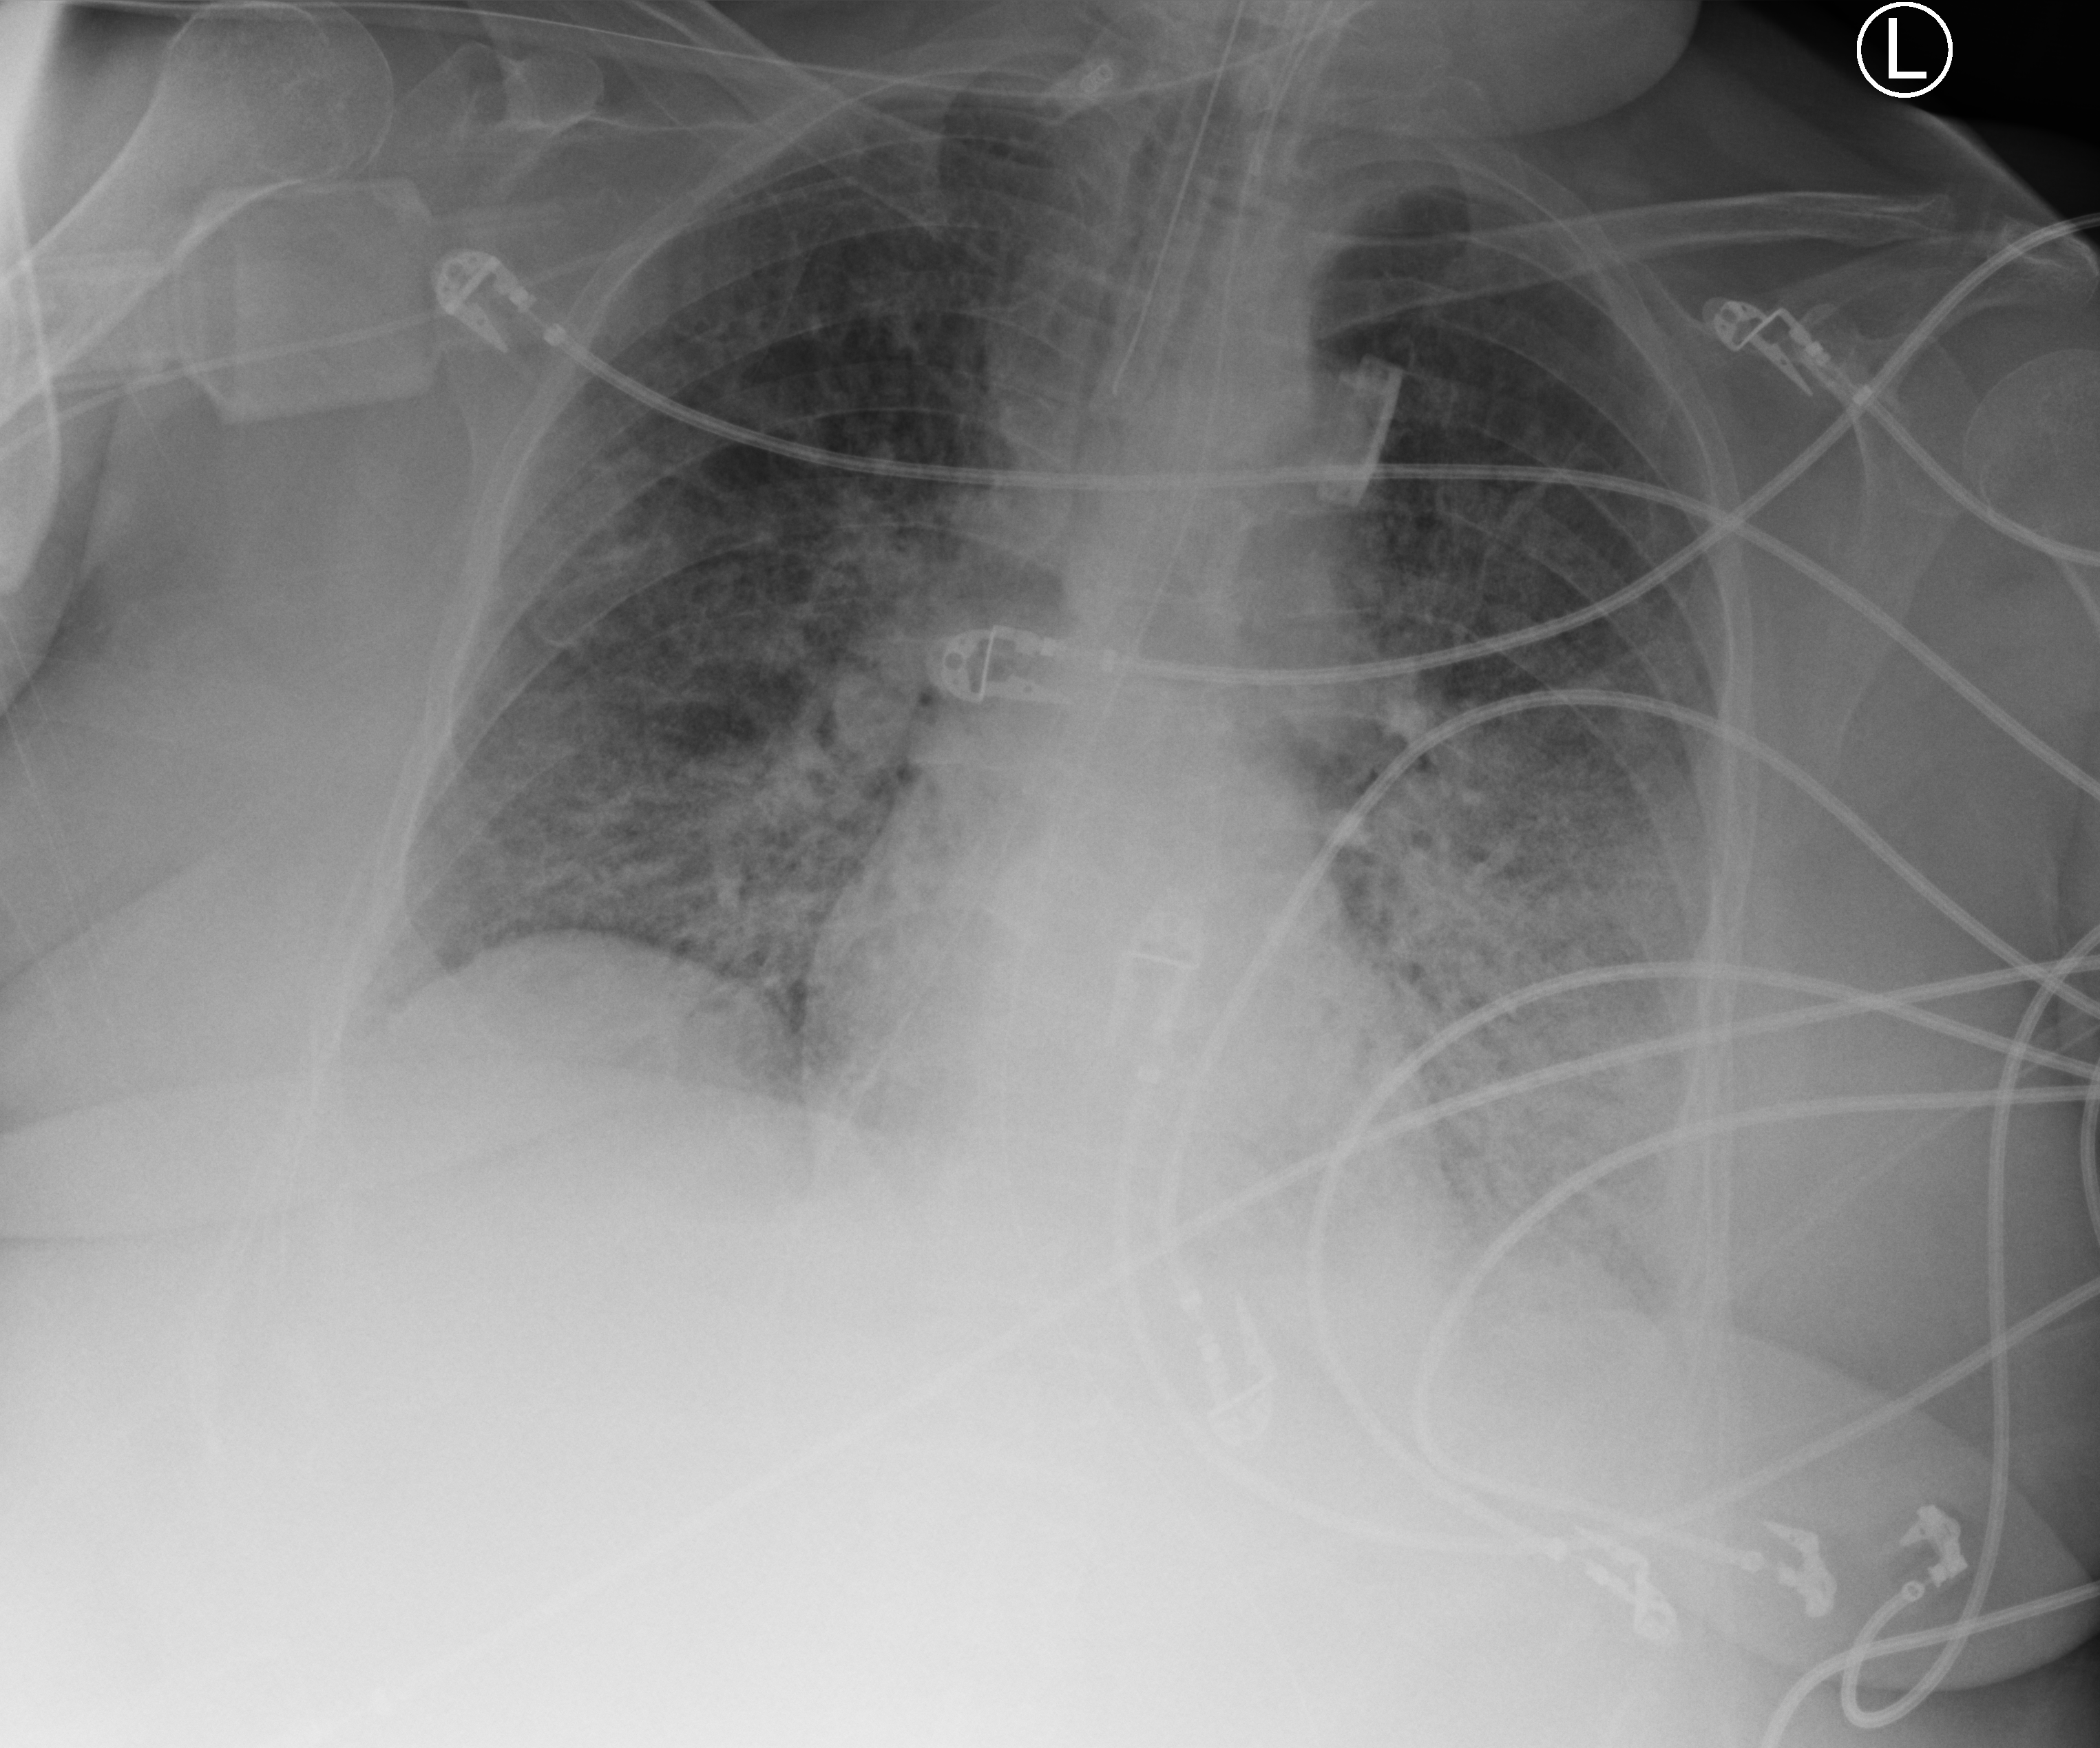
Chest X-ray (portable); anteroposterior (AP) projection. Patient hospitalised with COVID-19; female, aged 60–74 years.
From the hospital-stay record, not from the radiograph (when in the stay this image was taken is not recorded): mechanically ventilated during this hospital stay: yes.